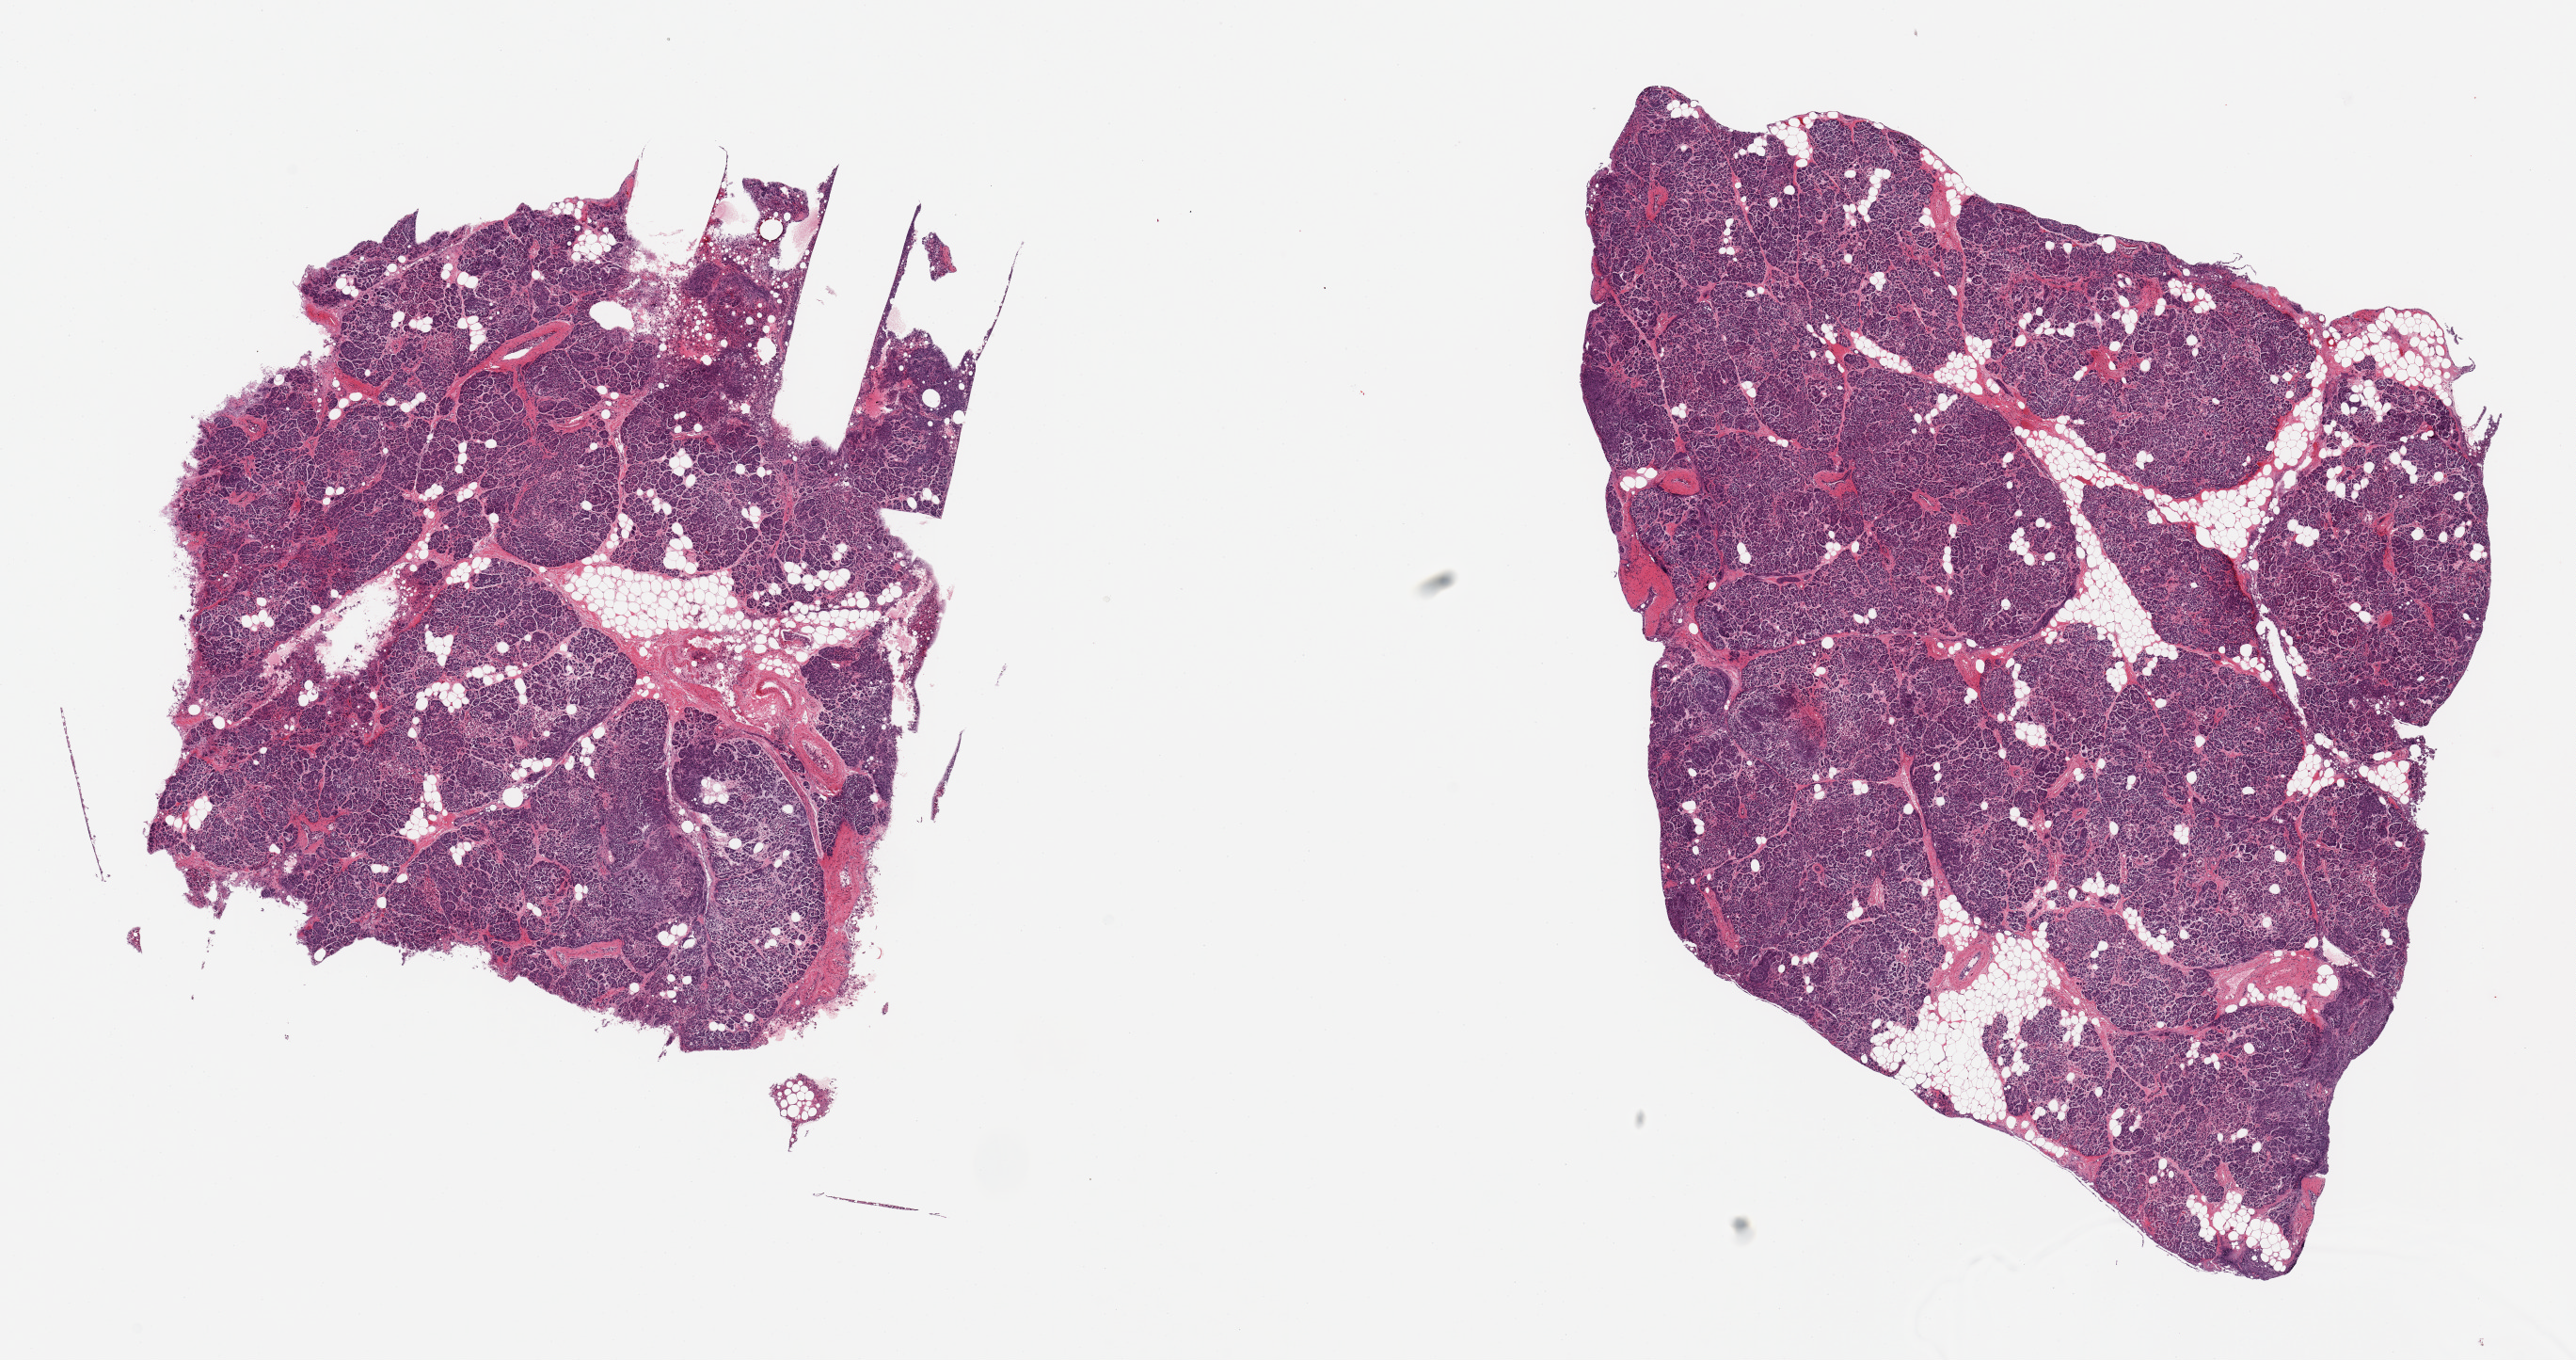
Digitized hematoxylin and eosin (H&E)-stained section, a low-resolution overview of the entire scanned area, about 21.7 x 11.4 mm (acquisition: 20x scan); PAXgene-fixed, paraffin-embedded tissue; section of pancreas (target tissue); donor tissue sample. Donor: male.
Reviewer comment on this tissue sample: 2 pieces, moderate-advanced autolysis, Islets generally degraded.